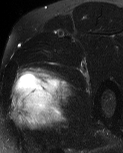
MRI of an extremity soft-tissue mass, one axial slice. Slice 42 of 60 in the series (ordered by position). T2-weighted fat-saturated. MR volume resampled by the dataset authors to the PET/CT grid (not the native acquisition matrix). 3.27 mm slice thickness. 123 × 153 image matrix, field of view 120 × 149 mm. Male patient. From the clinical record (not read from this slice): histological type: pleiomorphic liposarcoma; grade: high; site of the primary tumour: left thigh.
Structures marked on this image (expert contour drawn on MRI and transferred to this co-registered scan by the dataset authors):
- gross tumour volume including surrounding oedema: bounding box <11,68,71,131> (left, top, right, bottom; pixels)
- gross tumour volume (mass): <15,72,62,112>